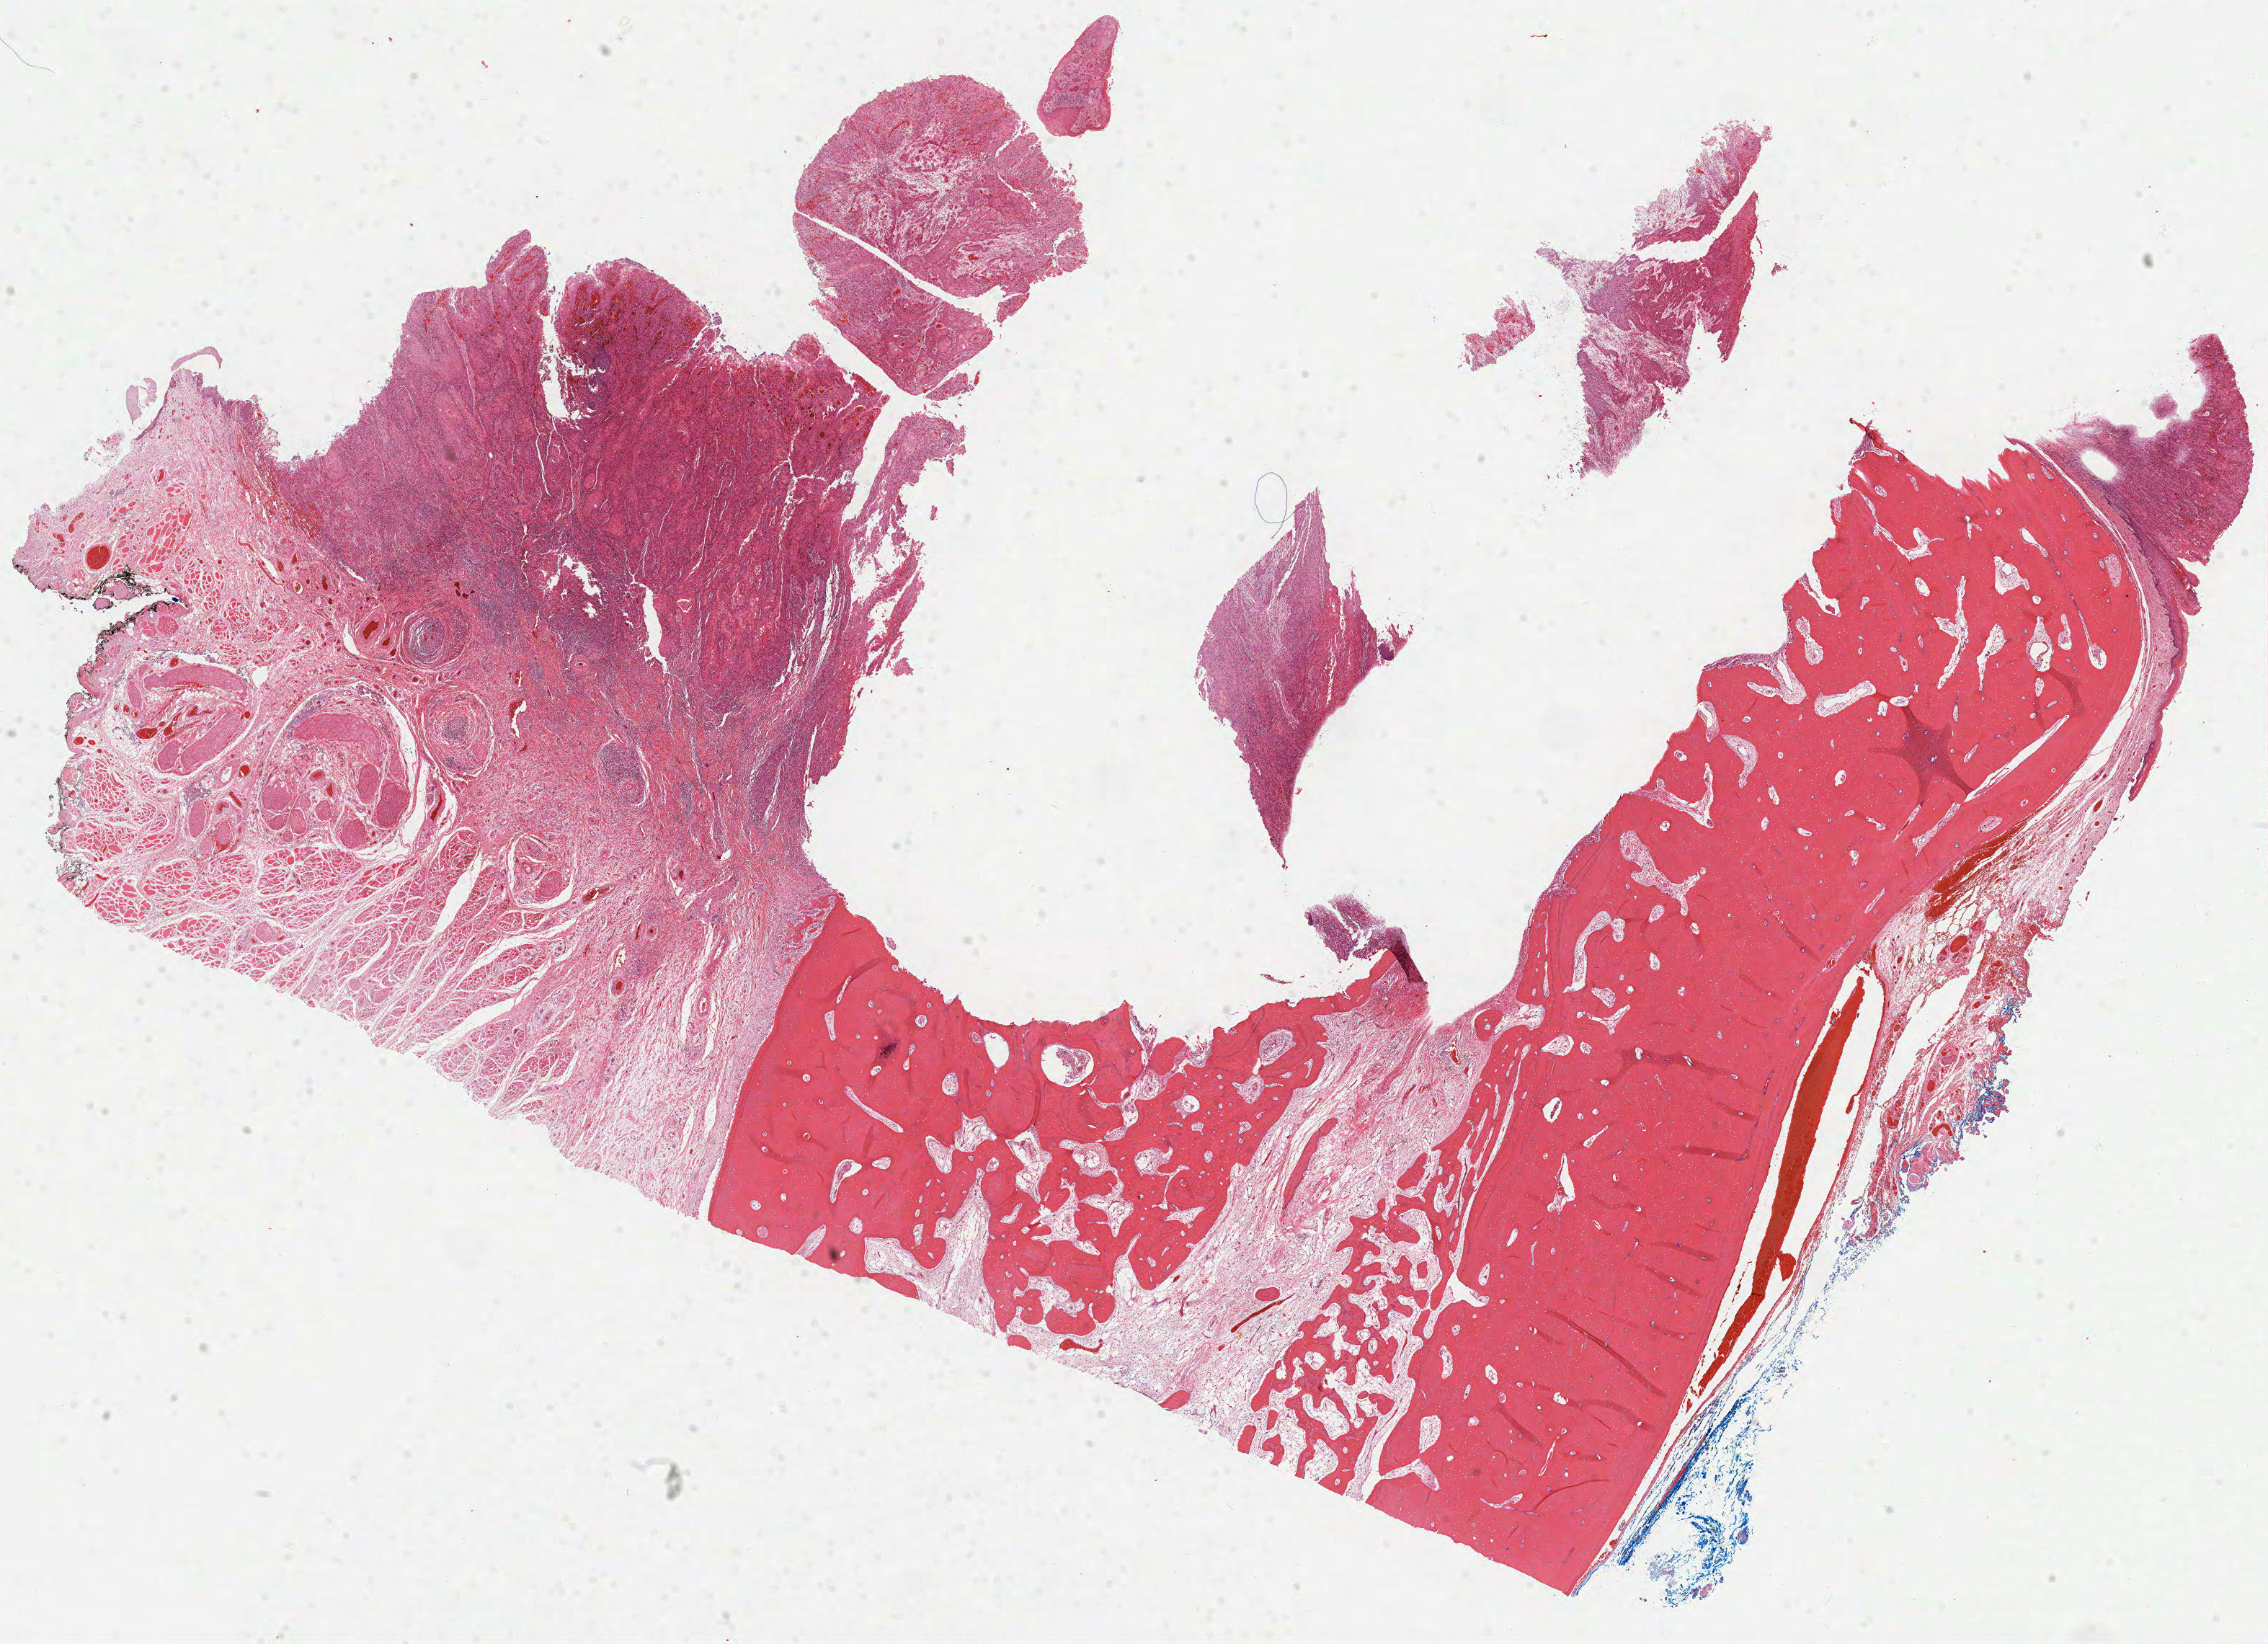
Digitized H&E-stained tissue section (whole slide) — a low-resolution overview of the entire scanned area, about 25.4 x 18.4 mm. Formalin-fixed paraffin-embedded (FFPE) diagnostic section. Head and neck, primary tumour sample. Patient: male, age at initial diagnosis 56 years.
Pathologic diagnosis: Squamous cell carcinoma, NOS (overlapping lesion of lip, oral cavity and pharynx).